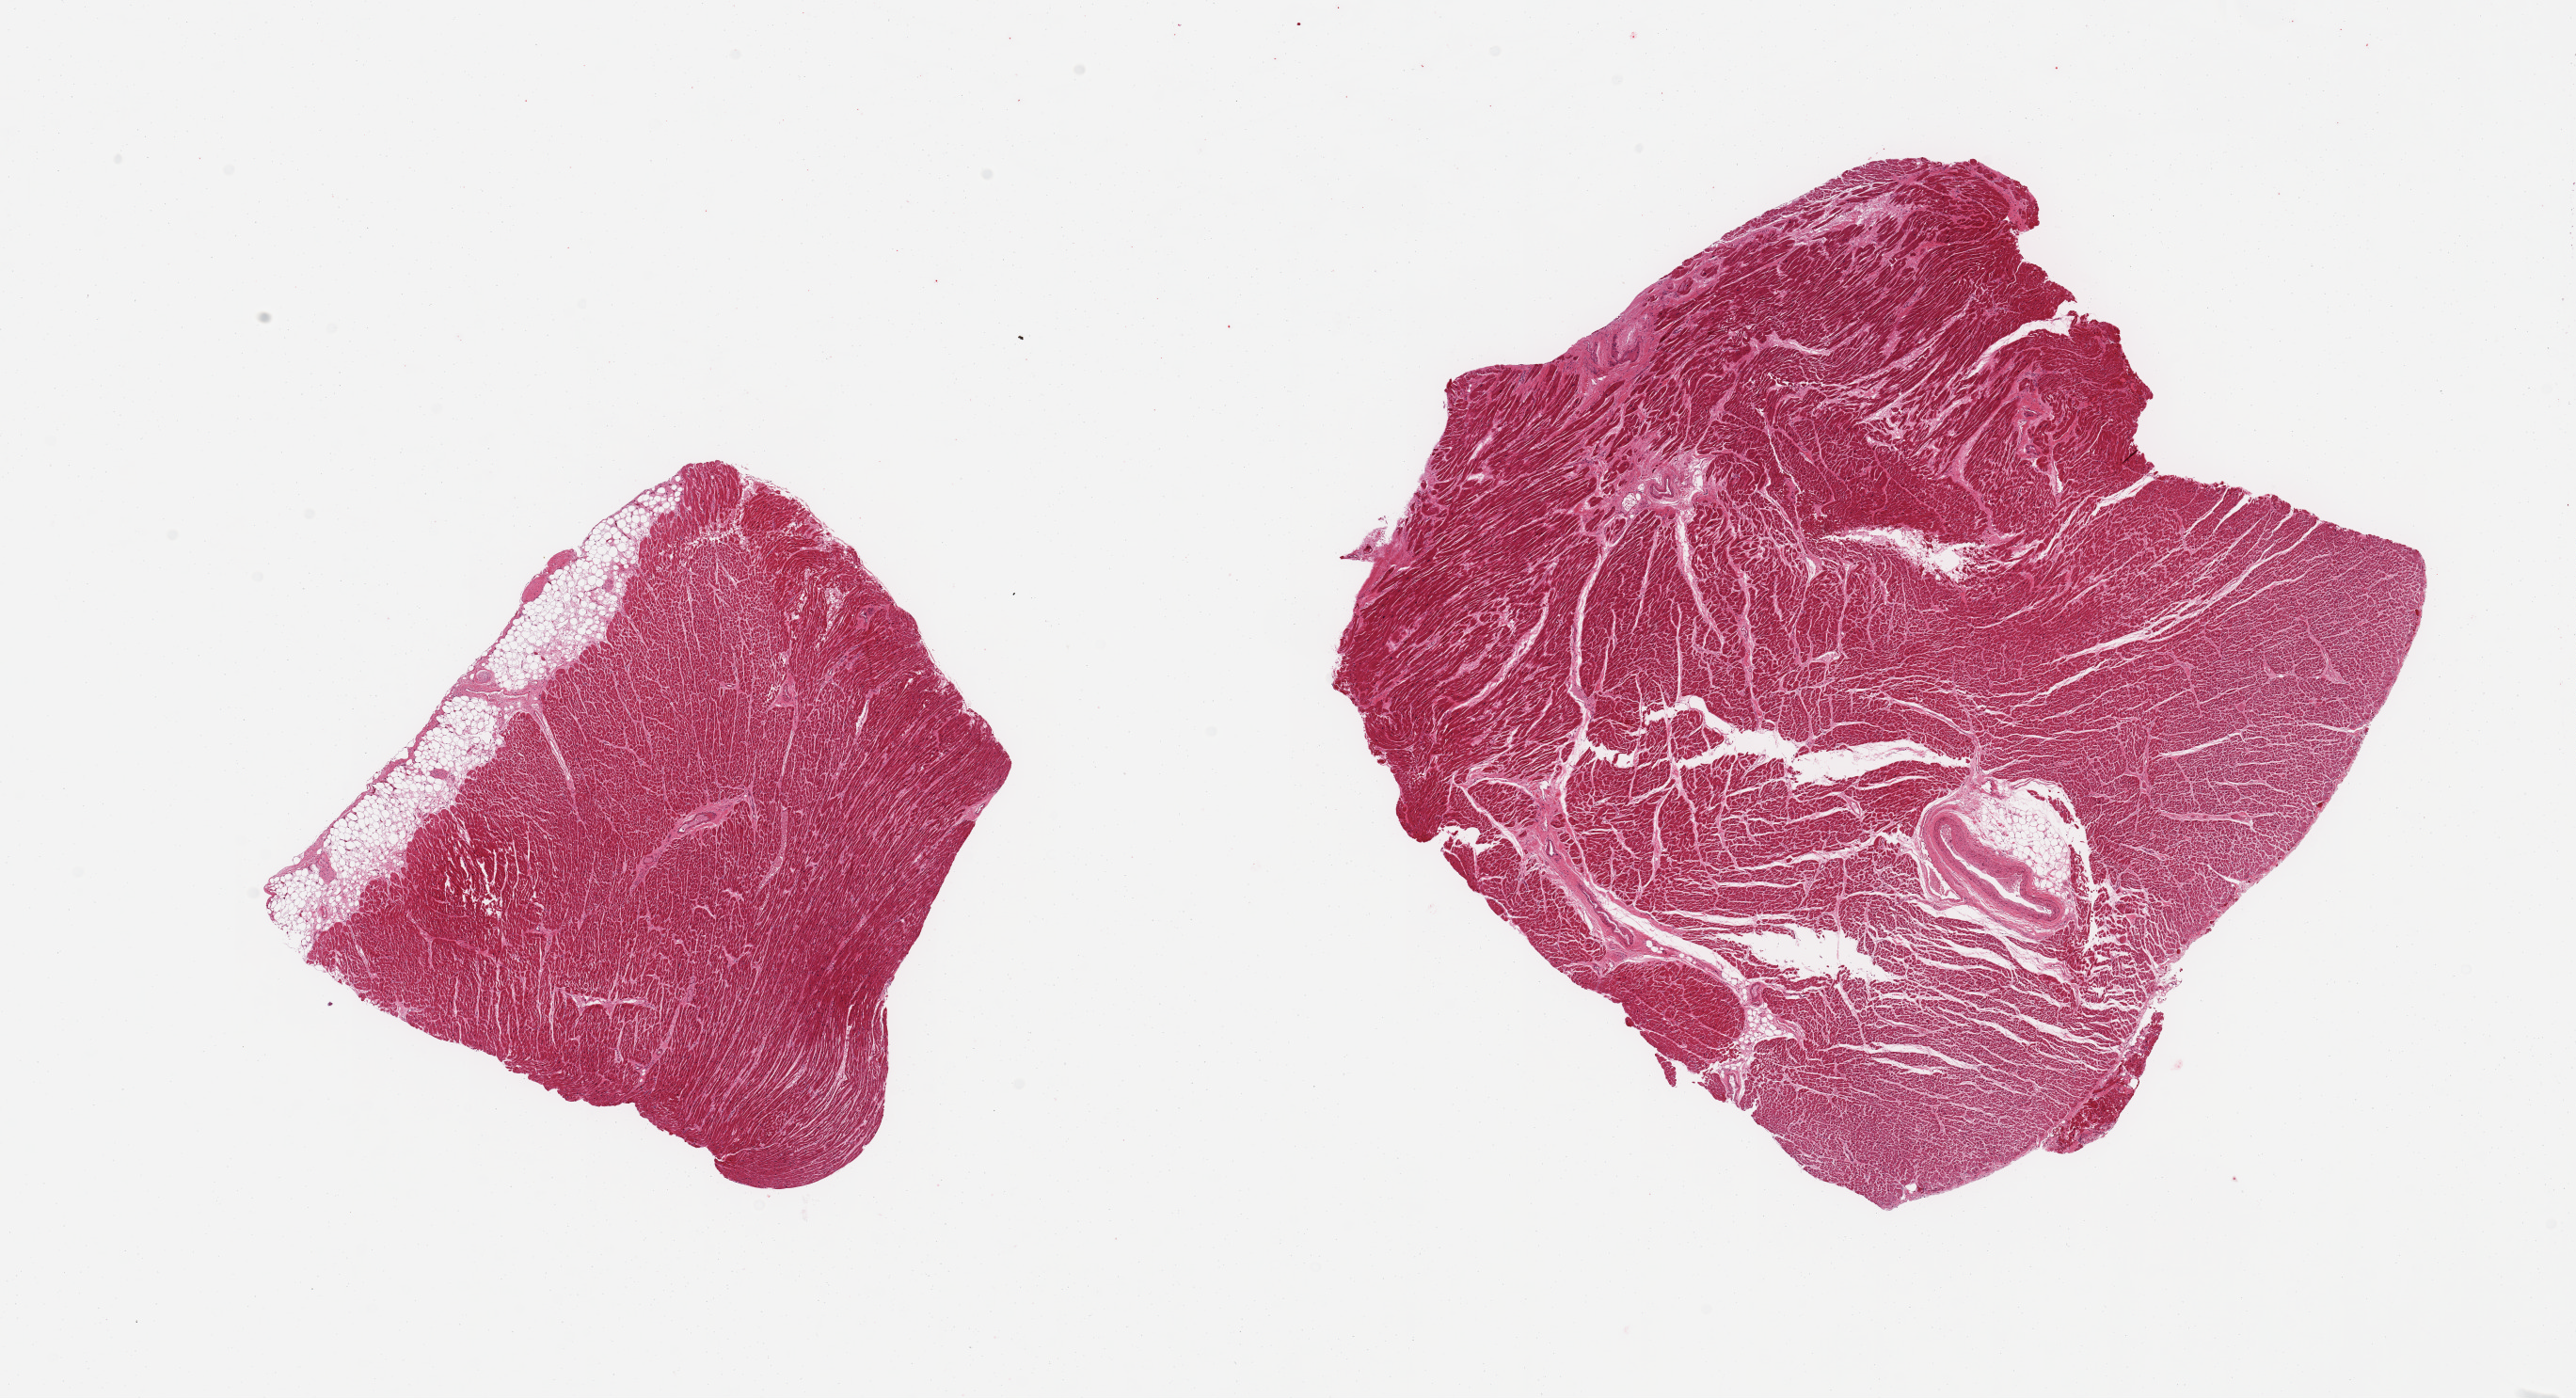
Whole-slide image, hematoxylin and eosin (H&E) stain — whole scanned area (about 21.7 x 11.8 mm, from a 20x scan) shown as a low-resolution overview; PAXgene-fixed, paraffin-embedded tissue; target tissue: heart; tissue donor sample.
• review note (as recorded): 2 pieces; 10% fibrofatty content